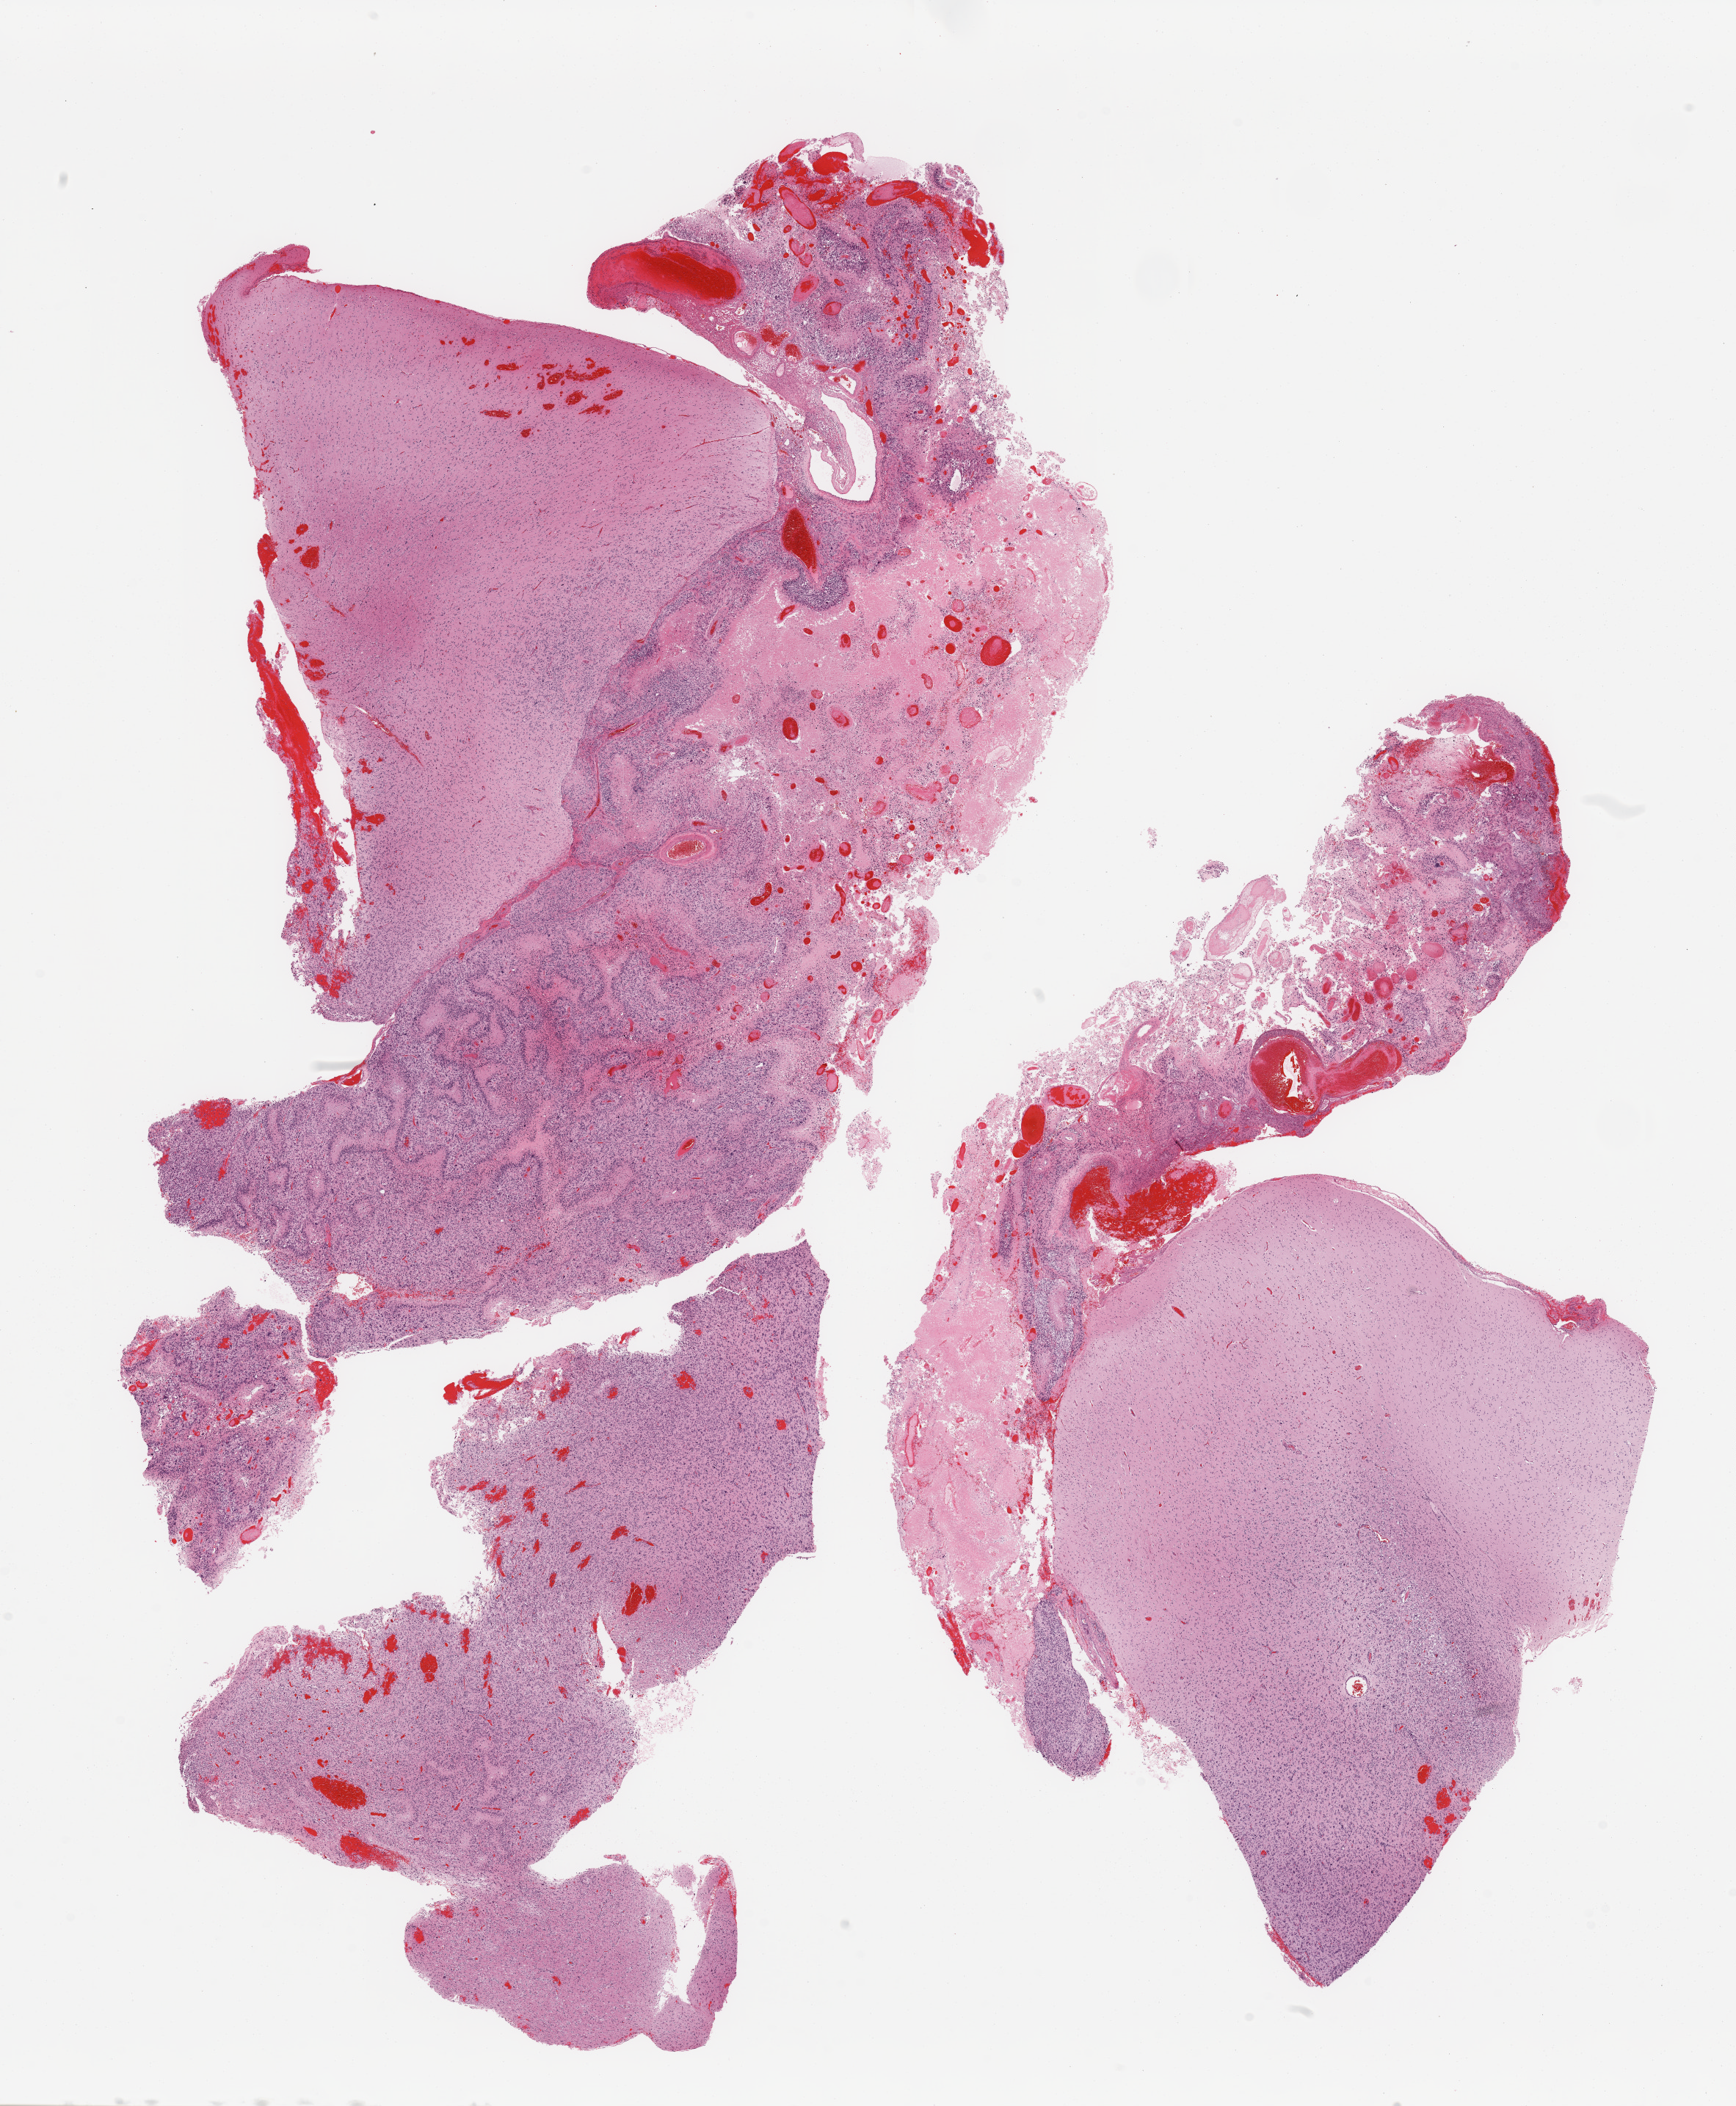
Digitized Hematoxylin and eosin (H&E) stained tissue section (whole slide), shown as a low-resolution overview of the whole scanned area (about 18.7 x 22.7 mm, slide scanned at 20x). Tumour tissue sample, sampled site: brain. Male, 58 y/o. Composition of this section per pathologist review: tumour nuclei 55%, necrosis 20%.
Primary tumour site (as recorded): temporal lobe. Histologic diagnosis: Glioblastoma.